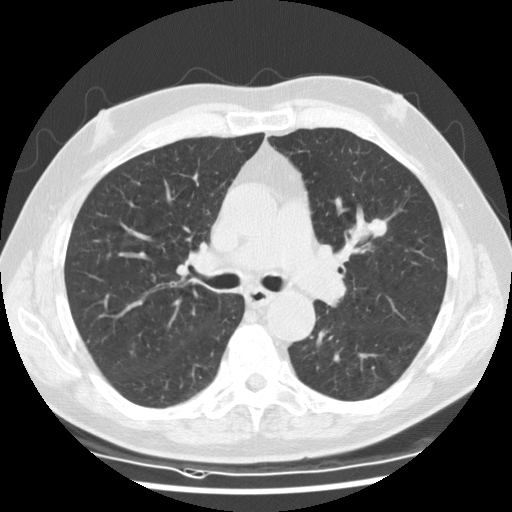
Low-dose screening chest CT, one axial slice; position 78 of 135 along the scan axis; reconstruction kernel STANDARD; 120 kVp; lung window (W 1500 / L -600 HU); 2.5 mm slice thickness; 512 × 512 image matrix, field of view 340 × 340 mm.
Structures marked on this image (expert manual segmentation):
- lesion 1 (tumor, upper lobe of left lung): bounding box [x1, y1, x2, y2] px = [368, 218, 388, 238]